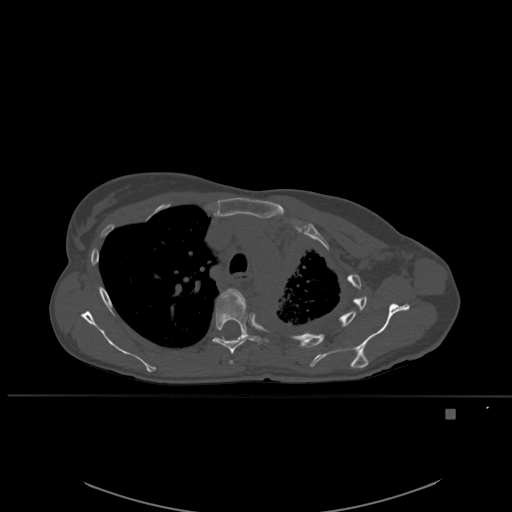
CT including the spine, one axial slice; slice 400 of 537 in the series (ordered by position); bone window (W 1800 / L 400 HU); 512 × 512 image matrix, field of view 440 × 440 mm. Female patient, age 45 years. Case-level facts recorded for this patient, not image findings: primary cancer: lung.
Outlined on this slice (semi-automatically segmented with operator editing):
- T4 vertebra: bounding box [x1, y1, x2, y2] px = [221, 288, 246, 365]
- T5 vertebra: [212, 289, 269, 354]